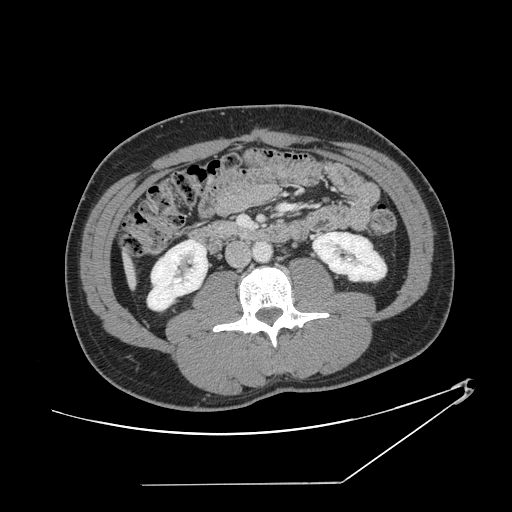
Contrast-enhanced abdominal CT, one axial slice. Position 39 of 152 along the scan axis. Reconstruction kernel STANDARD. 120 kVp. Intravenous contrast given. Soft-tissue window (W 400 / L 40 HU). 2.5 mm slice thickness. 512 × 512 image matrix, field of view 432 × 432 mm. Male patient, age 45 years. From the clinical record (not read from this slice): diagnosis: colorectal cancer liver metastases, imaged before liver resection.
Annotated regions visible in this slice (manually delineated by an expert):
- liver: bounding box <128,265,133,279> (left, top, right, bottom; pixels)
- planned liver remnant (the part of the liver to remain after resection): <129,266,133,276>